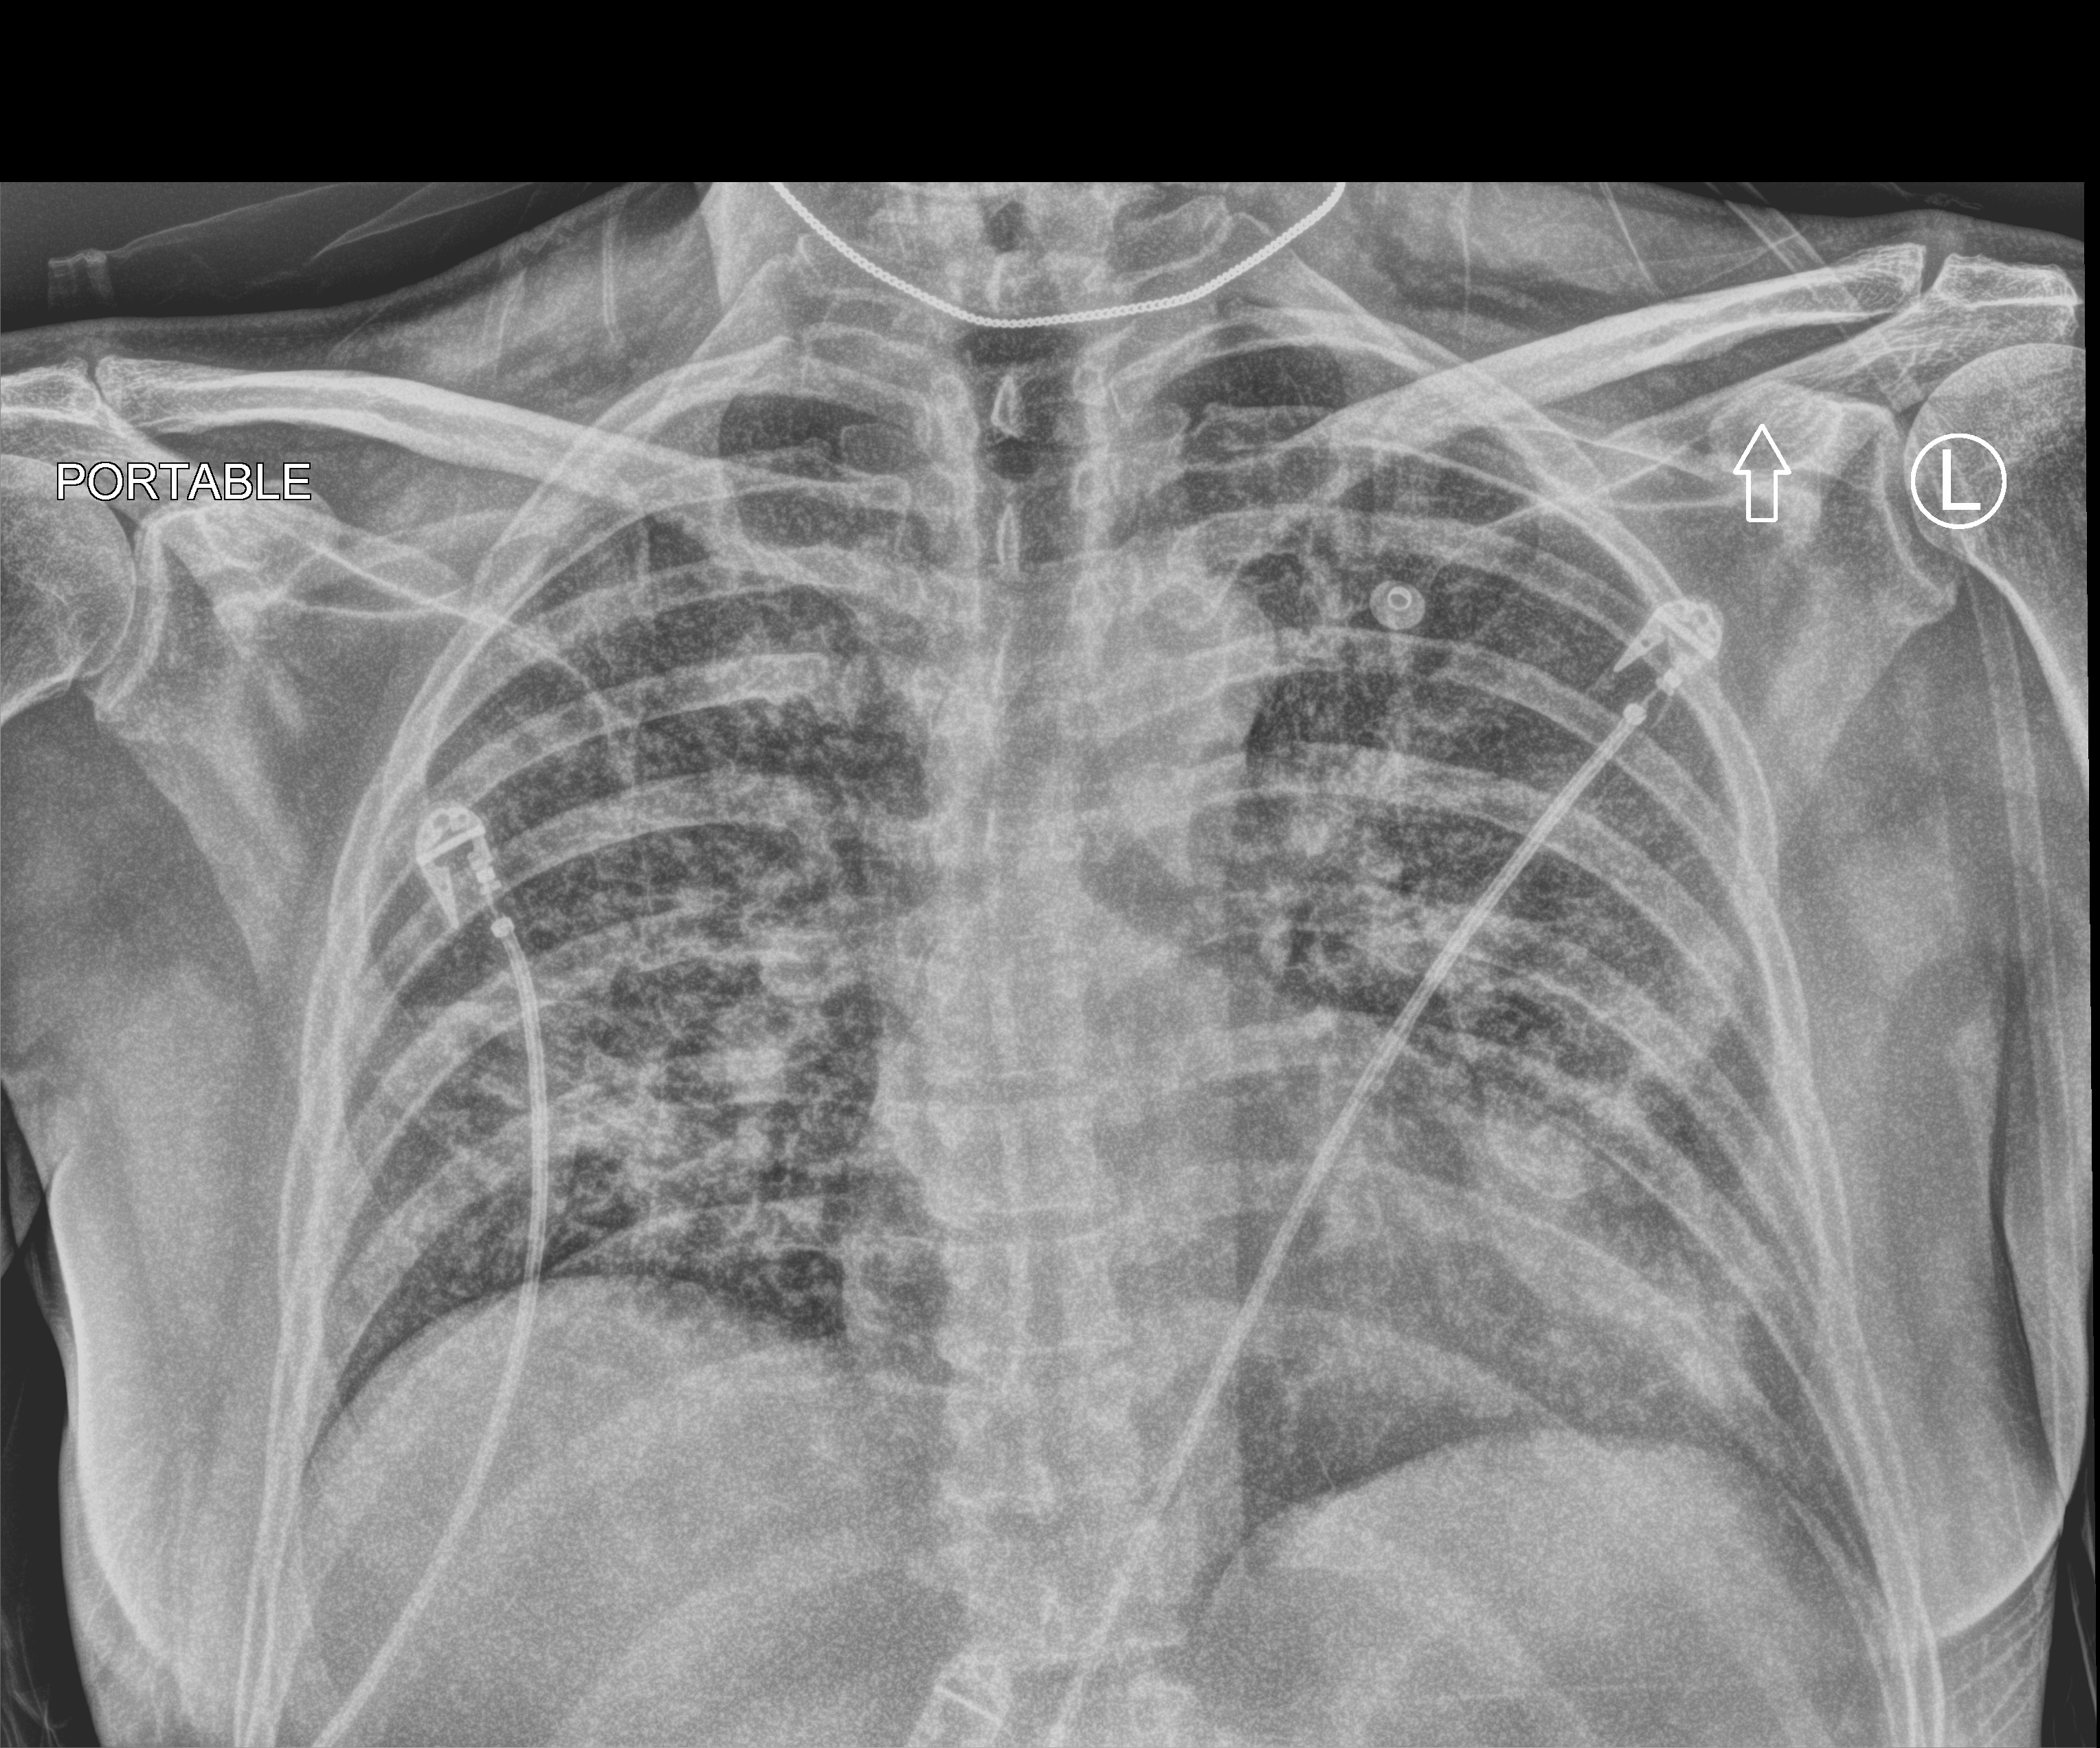
Bedside chest radiograph (computed radiography); anteroposterior (AP) projection. Male patient hospitalised with COVID-19, age 60–74 years.
From the hospital-stay record, not from the radiograph (when in the stay this image was taken is not recorded): admitted to intensive care during this hospital stay: no; mechanically ventilated during this hospital stay: no.